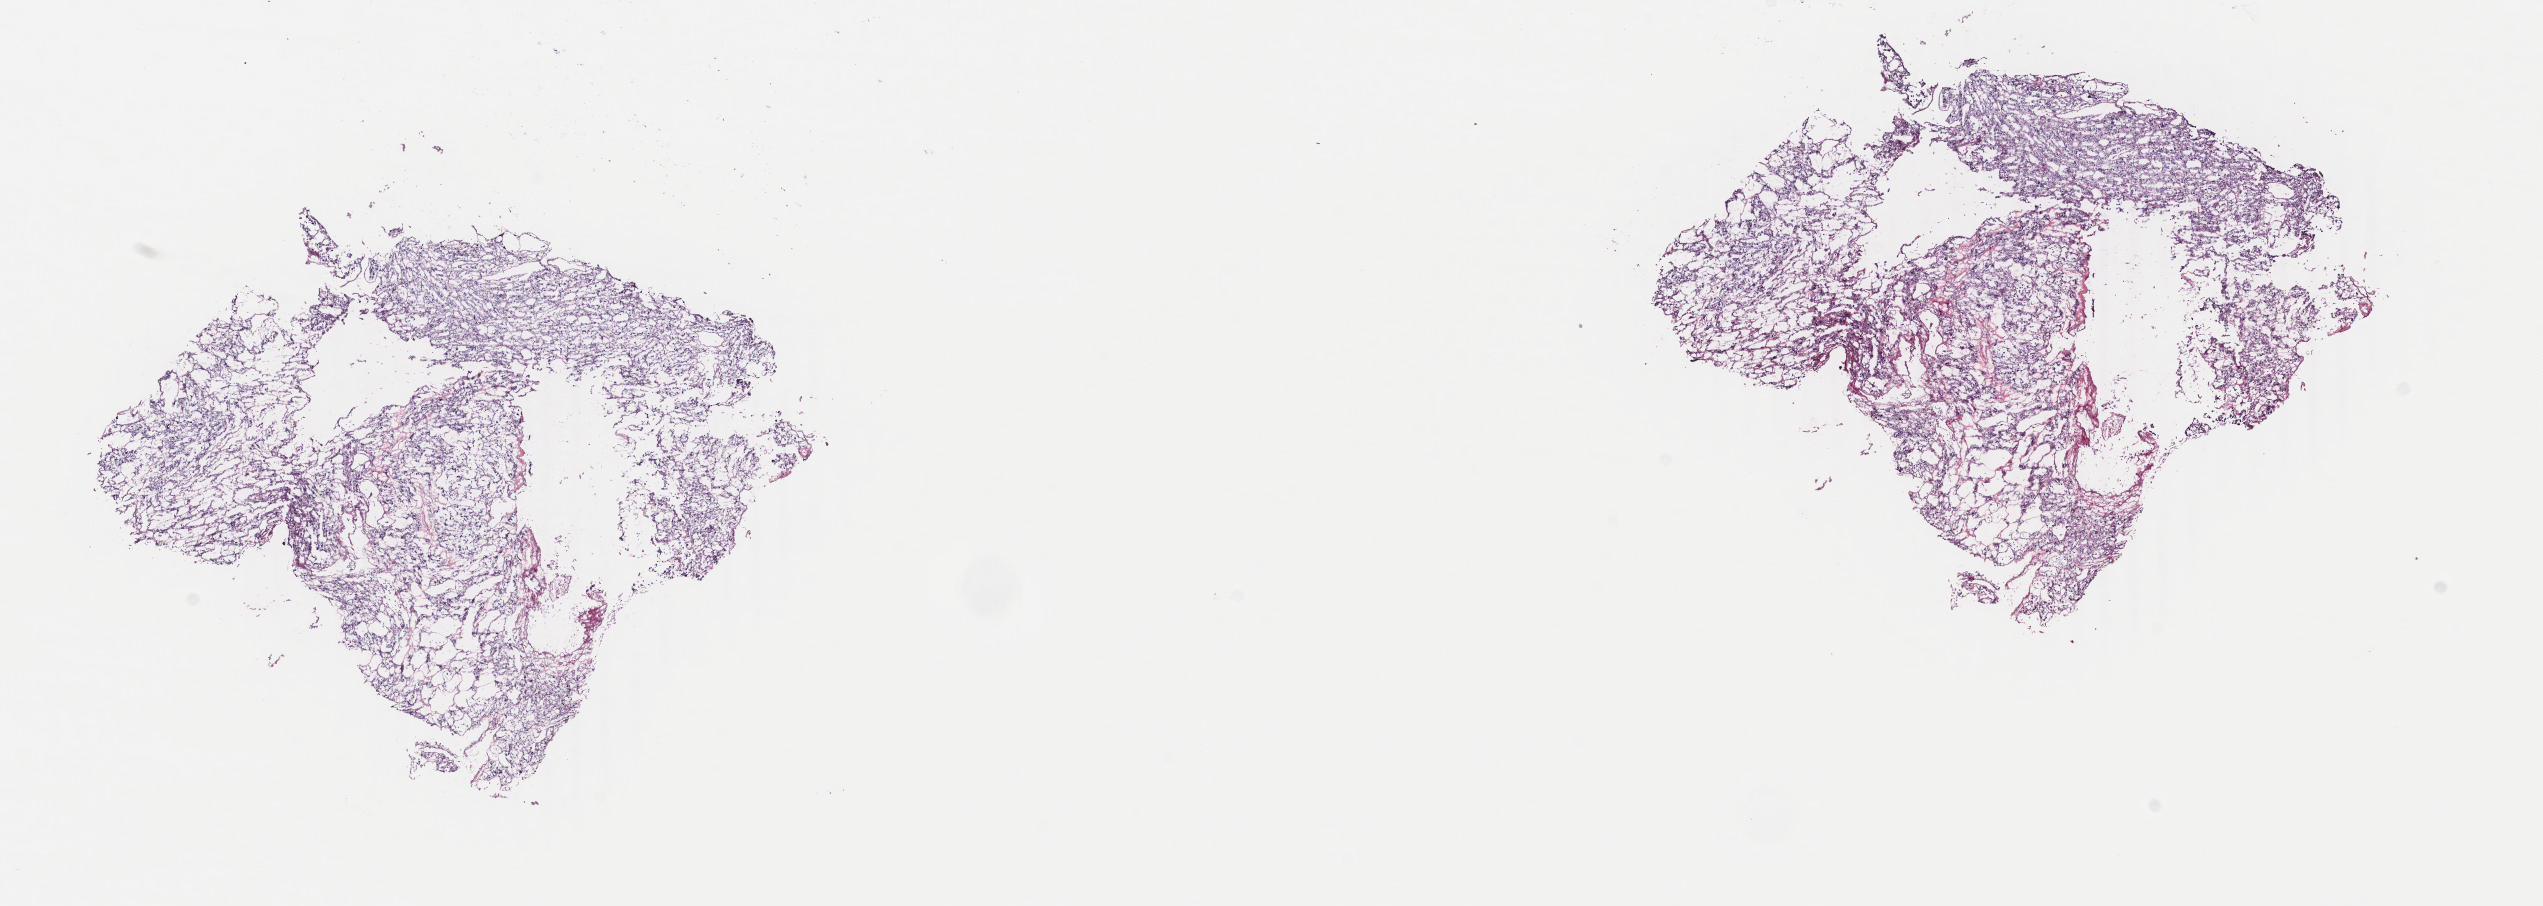
H&E whole-slide image — low-resolution overview of the scanned area, about 20.2 x 7.2 mm (from a 40x scan), frozen section from the top of the tissue portion, adrenal gland, primary tumour sample. Patient: female, age at initial diagnosis 30 years. Slide review estimates, as recorded: tumour cells 100%, tumour nuclei 95%, normal cells 0%, stromal cells 0%, necrosis 0%. Infiltration values recorded for this section: lymphocyte infiltration 0%, monocyte infiltration 0%, neutrophil infiltration 0%.
• laterality: left
• histologic diagnosis: Pheochromocytoma, NOS